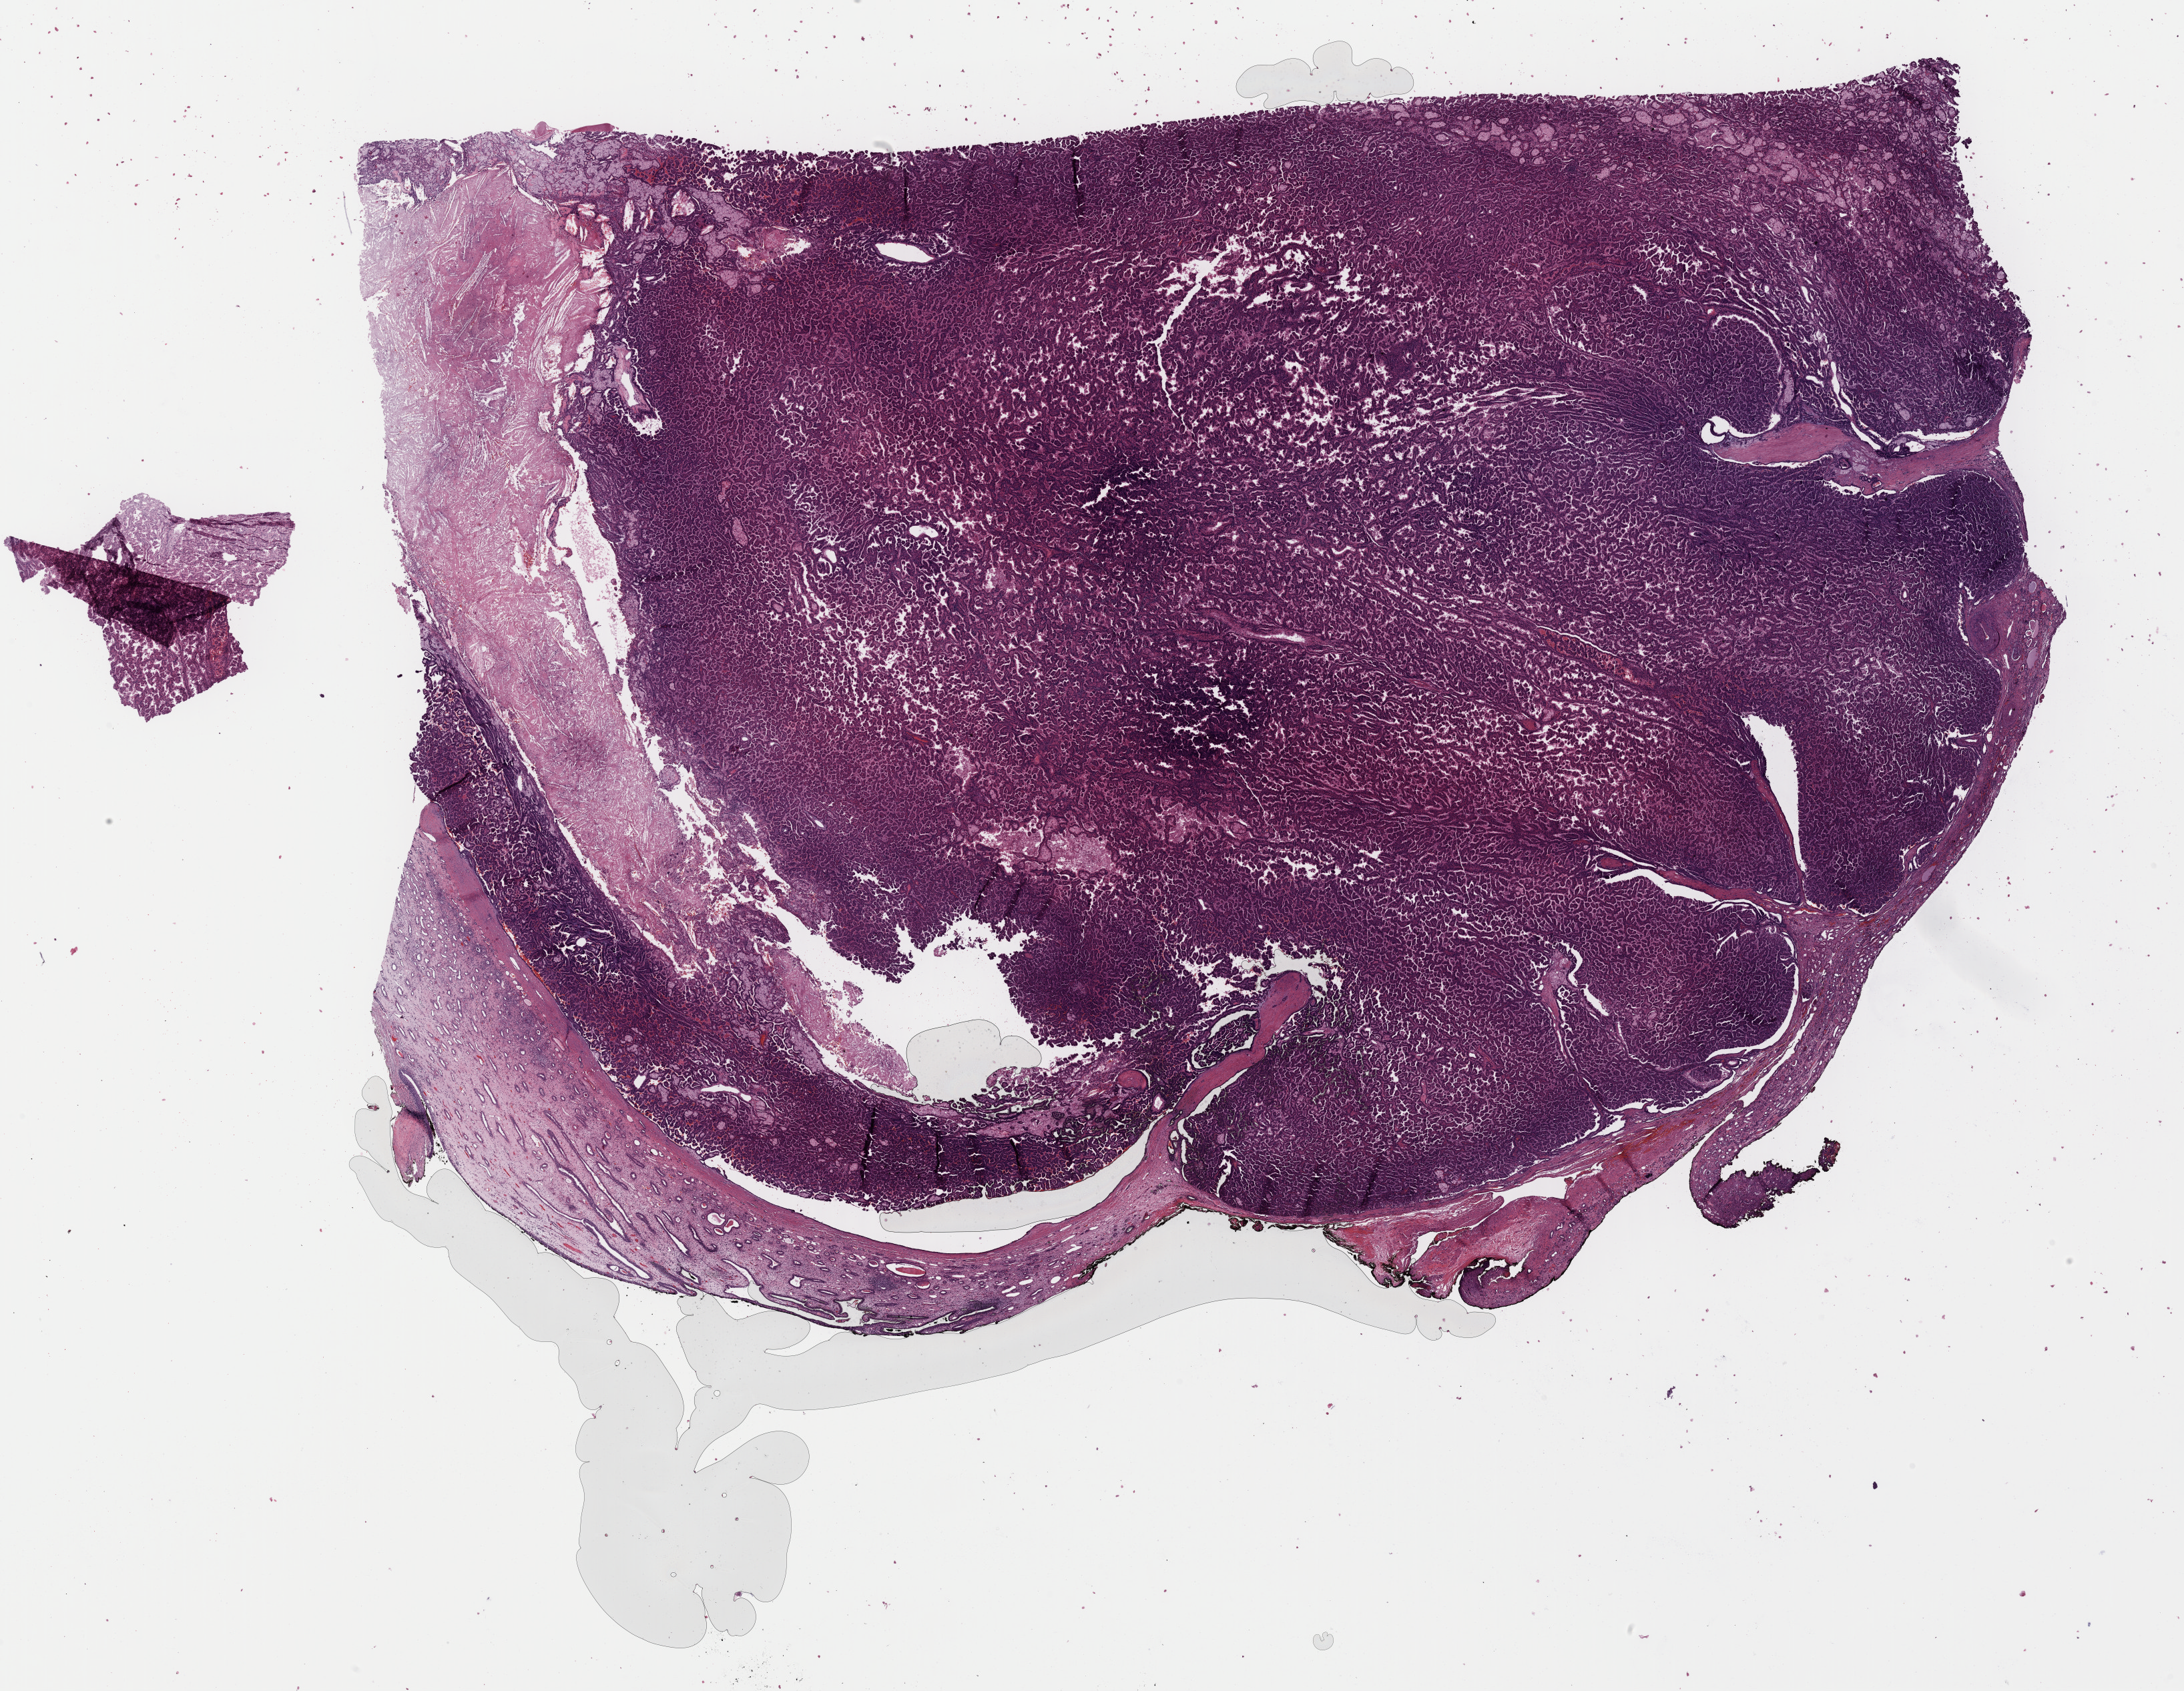
Digitized H&E-stained tissue section (whole slide), a low-resolution overview of the entire scanned area, about 25.8 x 20.0 mm (from a 40x scan), formalin-fixed paraffin-embedded (FFPE) diagnostic section, sample: primary tumour, kidney. Female patient; age at initial diagnosis 80 years.
Laterality: left. AJCC pathologic stage: I (7th edition). Histologic diagnosis: Papillary adenocarcinoma, NOS.